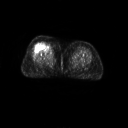
FDG PET of an extremity soft-tissue mass (from a PET/CT study), one axial slice. Position 24 of 267 along the scan axis. 3.27 mm slice thickness. 128 × 128 image matrix. Patient: female, 56 years. Case-level facts recorded for this patient, not image findings: histological type: malignant solitary fibrous tumor; grade: intermediate; site of the primary tumour: right thigh.
Structures marked on this image (expert contour drawn on MRI and transferred to this co-registered scan by the dataset authors):
- gross tumour volume including surrounding oedema: box from (x=37, y=41) to (x=54, y=54) px
- gross tumour volume (mass): (x=38, y=44)–(x=50, y=52)